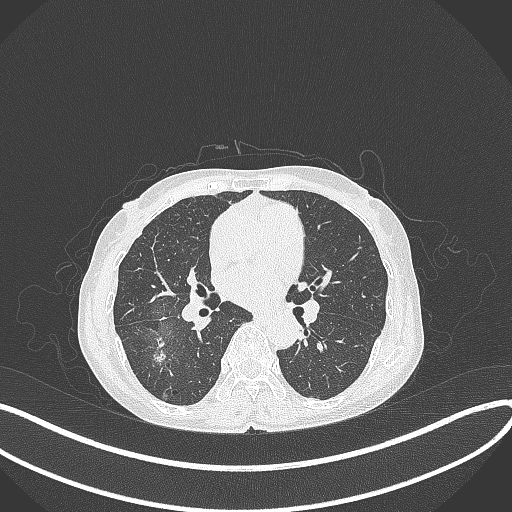
Chest CT, one axial slice; slice 202 of 371 in the series (ordered by position); reconstruction kernel B70f; 120 kVp; lung window (W 1500 / L -600 HU); 1 mm slice thickness; 512 × 512 image matrix. Female patient, age 69 years. Case-level facts recorded for this patient, not image findings: clinical TNM (as recorded): T1b N0 M0.
Outlined on this slice (rectangle marked by the reading radiologist):
- lung tumour (recorded histology: adenocarcinoma): bounding box (x1, y1, x2, y2) in pixels: (151, 339, 172, 371)